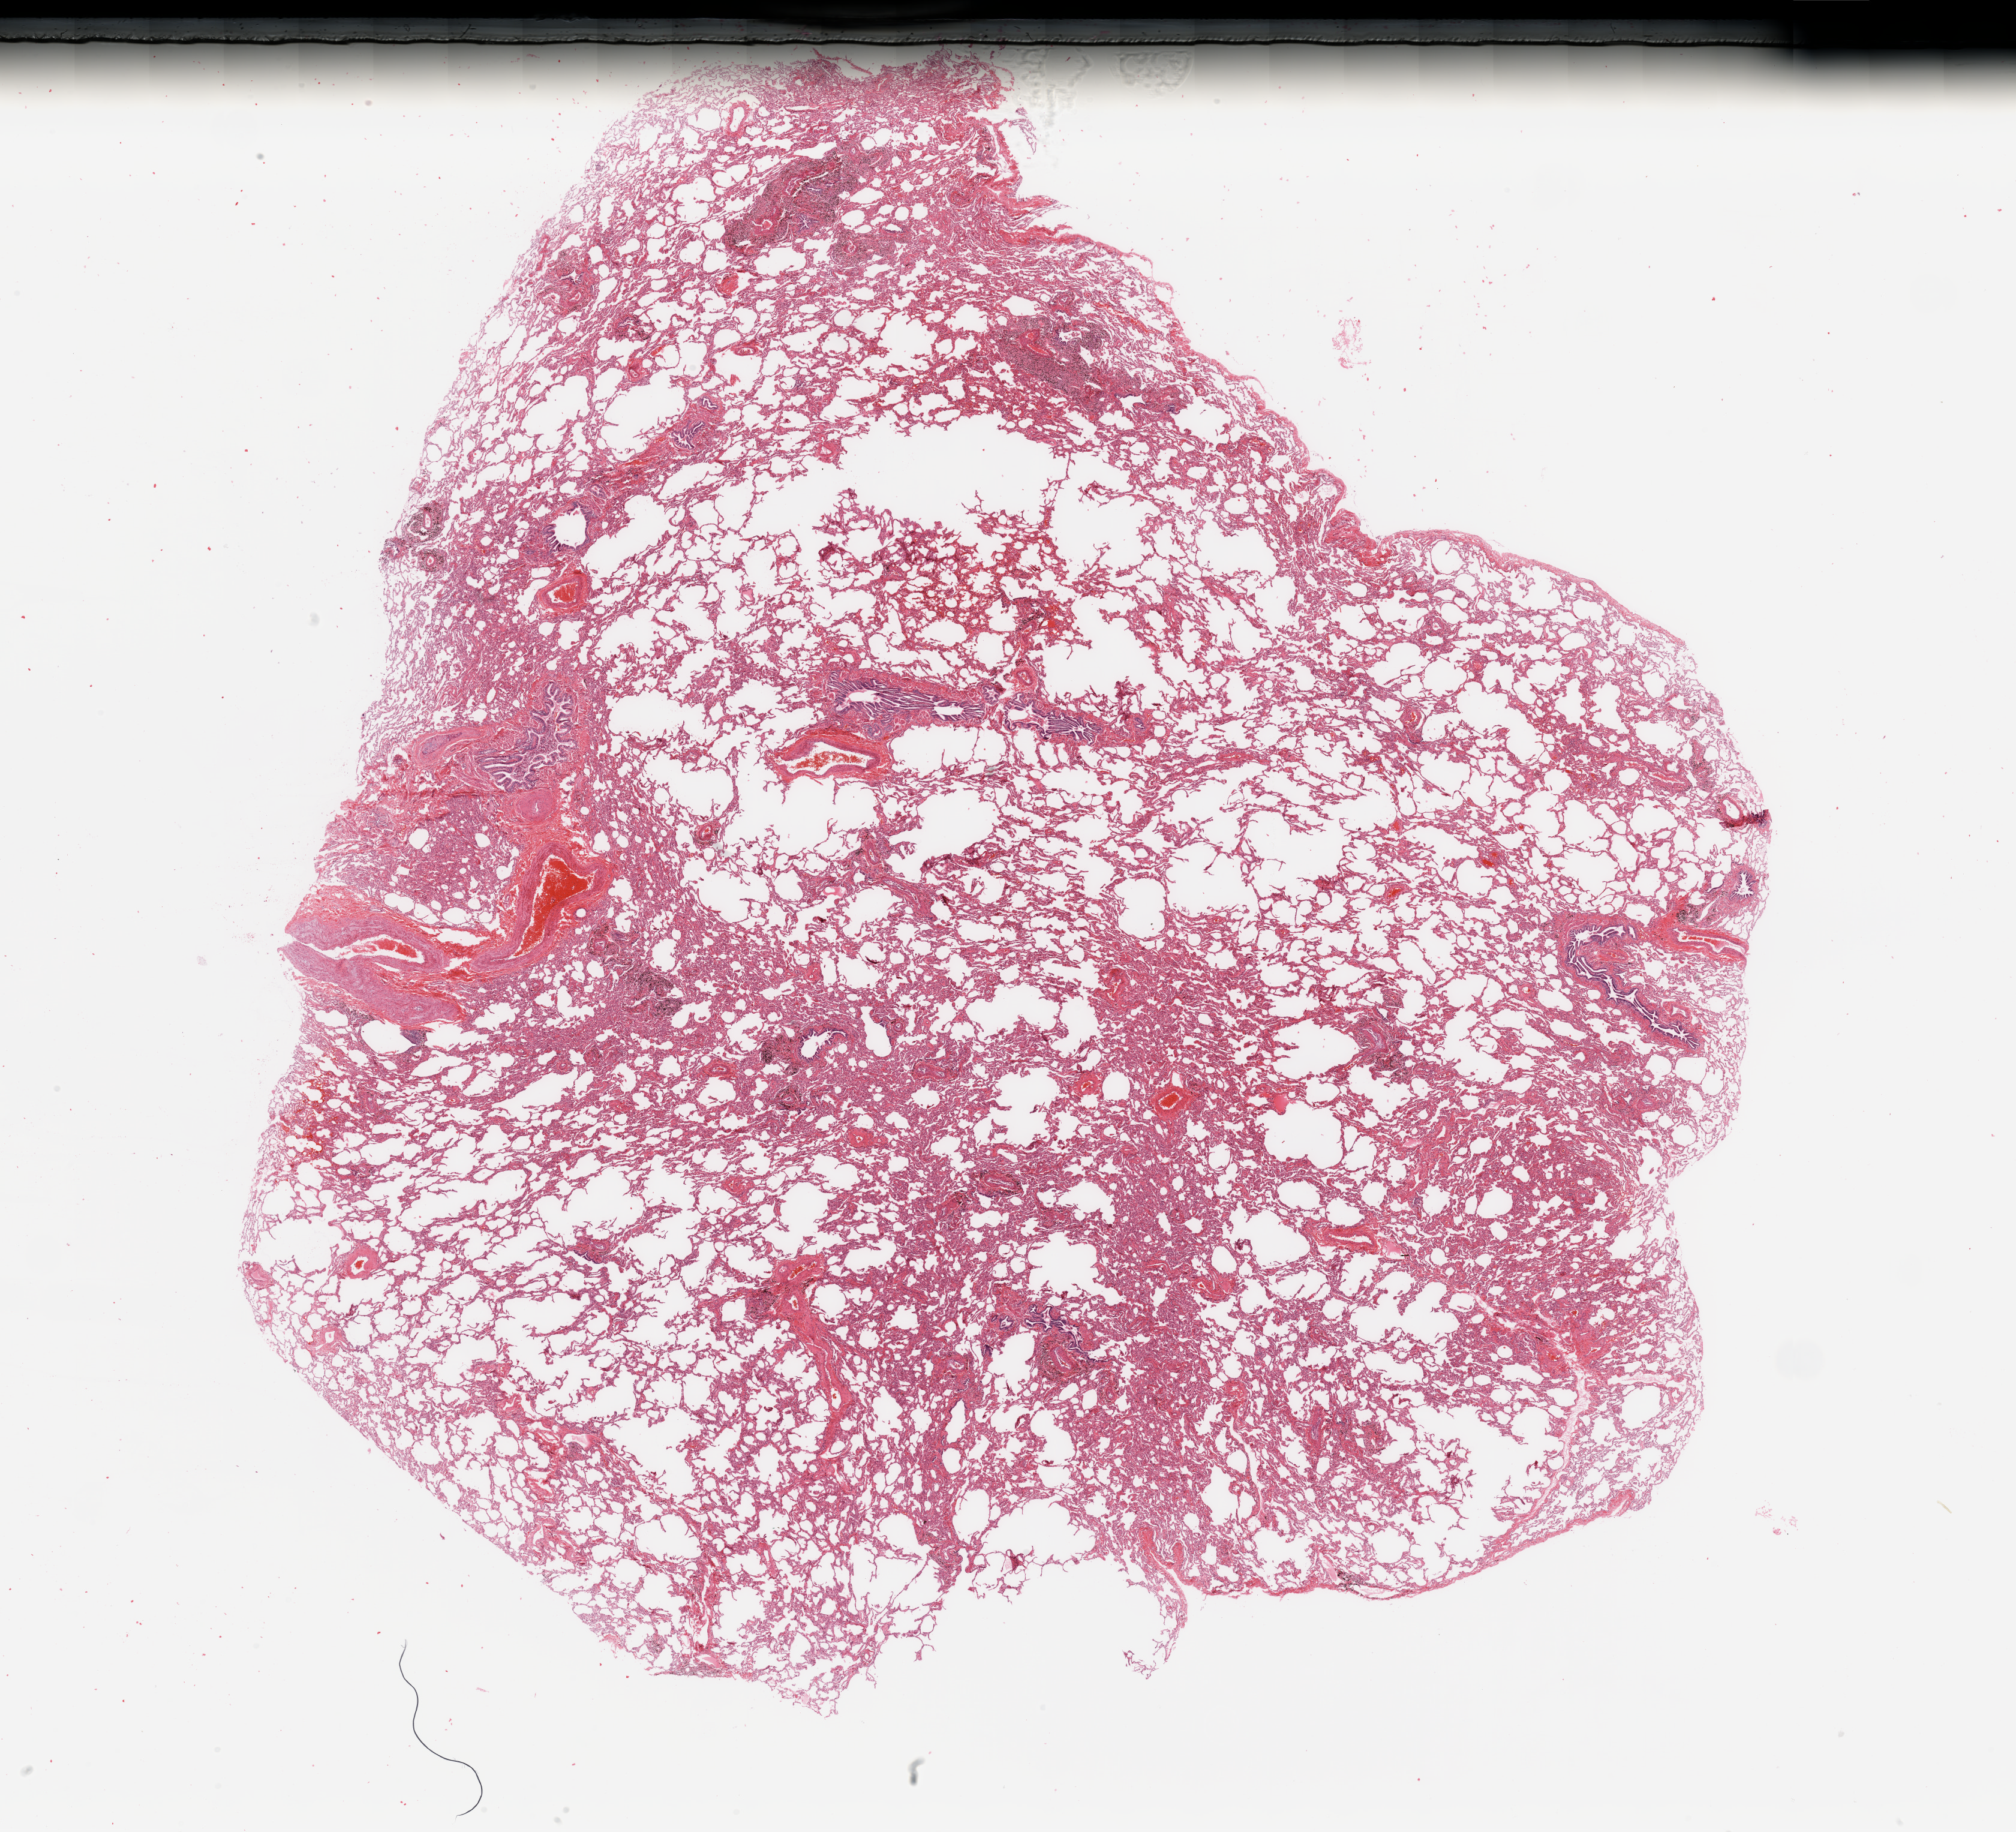
H&E-stained whole-slide image — low-resolution overview of the scanned area, about 26.6 x 24.2 mm; lung, normal (non-tumour) tissue. 61-year-old female patient.
* this section: normal (non-tumour) tissue from the same patient
* patient diagnosis: Adenocarcinoma, NOS